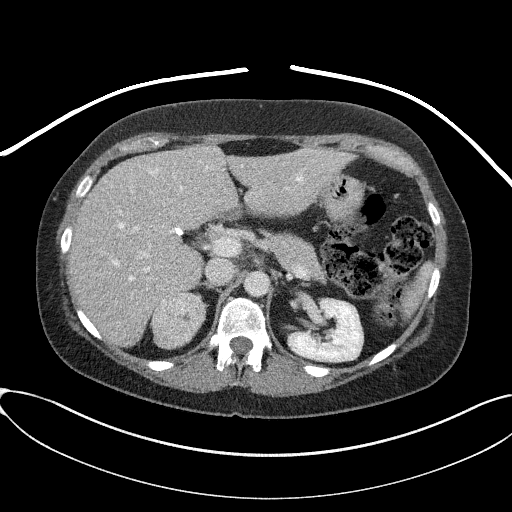
Contrast-enhanced abdominal CT, one axial slice; position 53 of 95 along the scan axis; reconstruction kernel I41f/2; soft-tissue window (W 400 / L 40 HU); 3 mm slice thickness; 512 × 512 image matrix, field of view 410 × 410 mm. Female patient, age 46 years. Case-level facts recorded for this patient, not image findings: diagnosis: adrenocortical carcinoma; tumour side: right adrenal; tumour size at pathology: 7.2 cm; Ki-67 index: 50 %; stage (as recorded): 4.
Outlined on this slice (semi-automatically segmented with operator editing):
- mass: bounding box <153,293,204,349> (left, top, right, bottom; pixels)